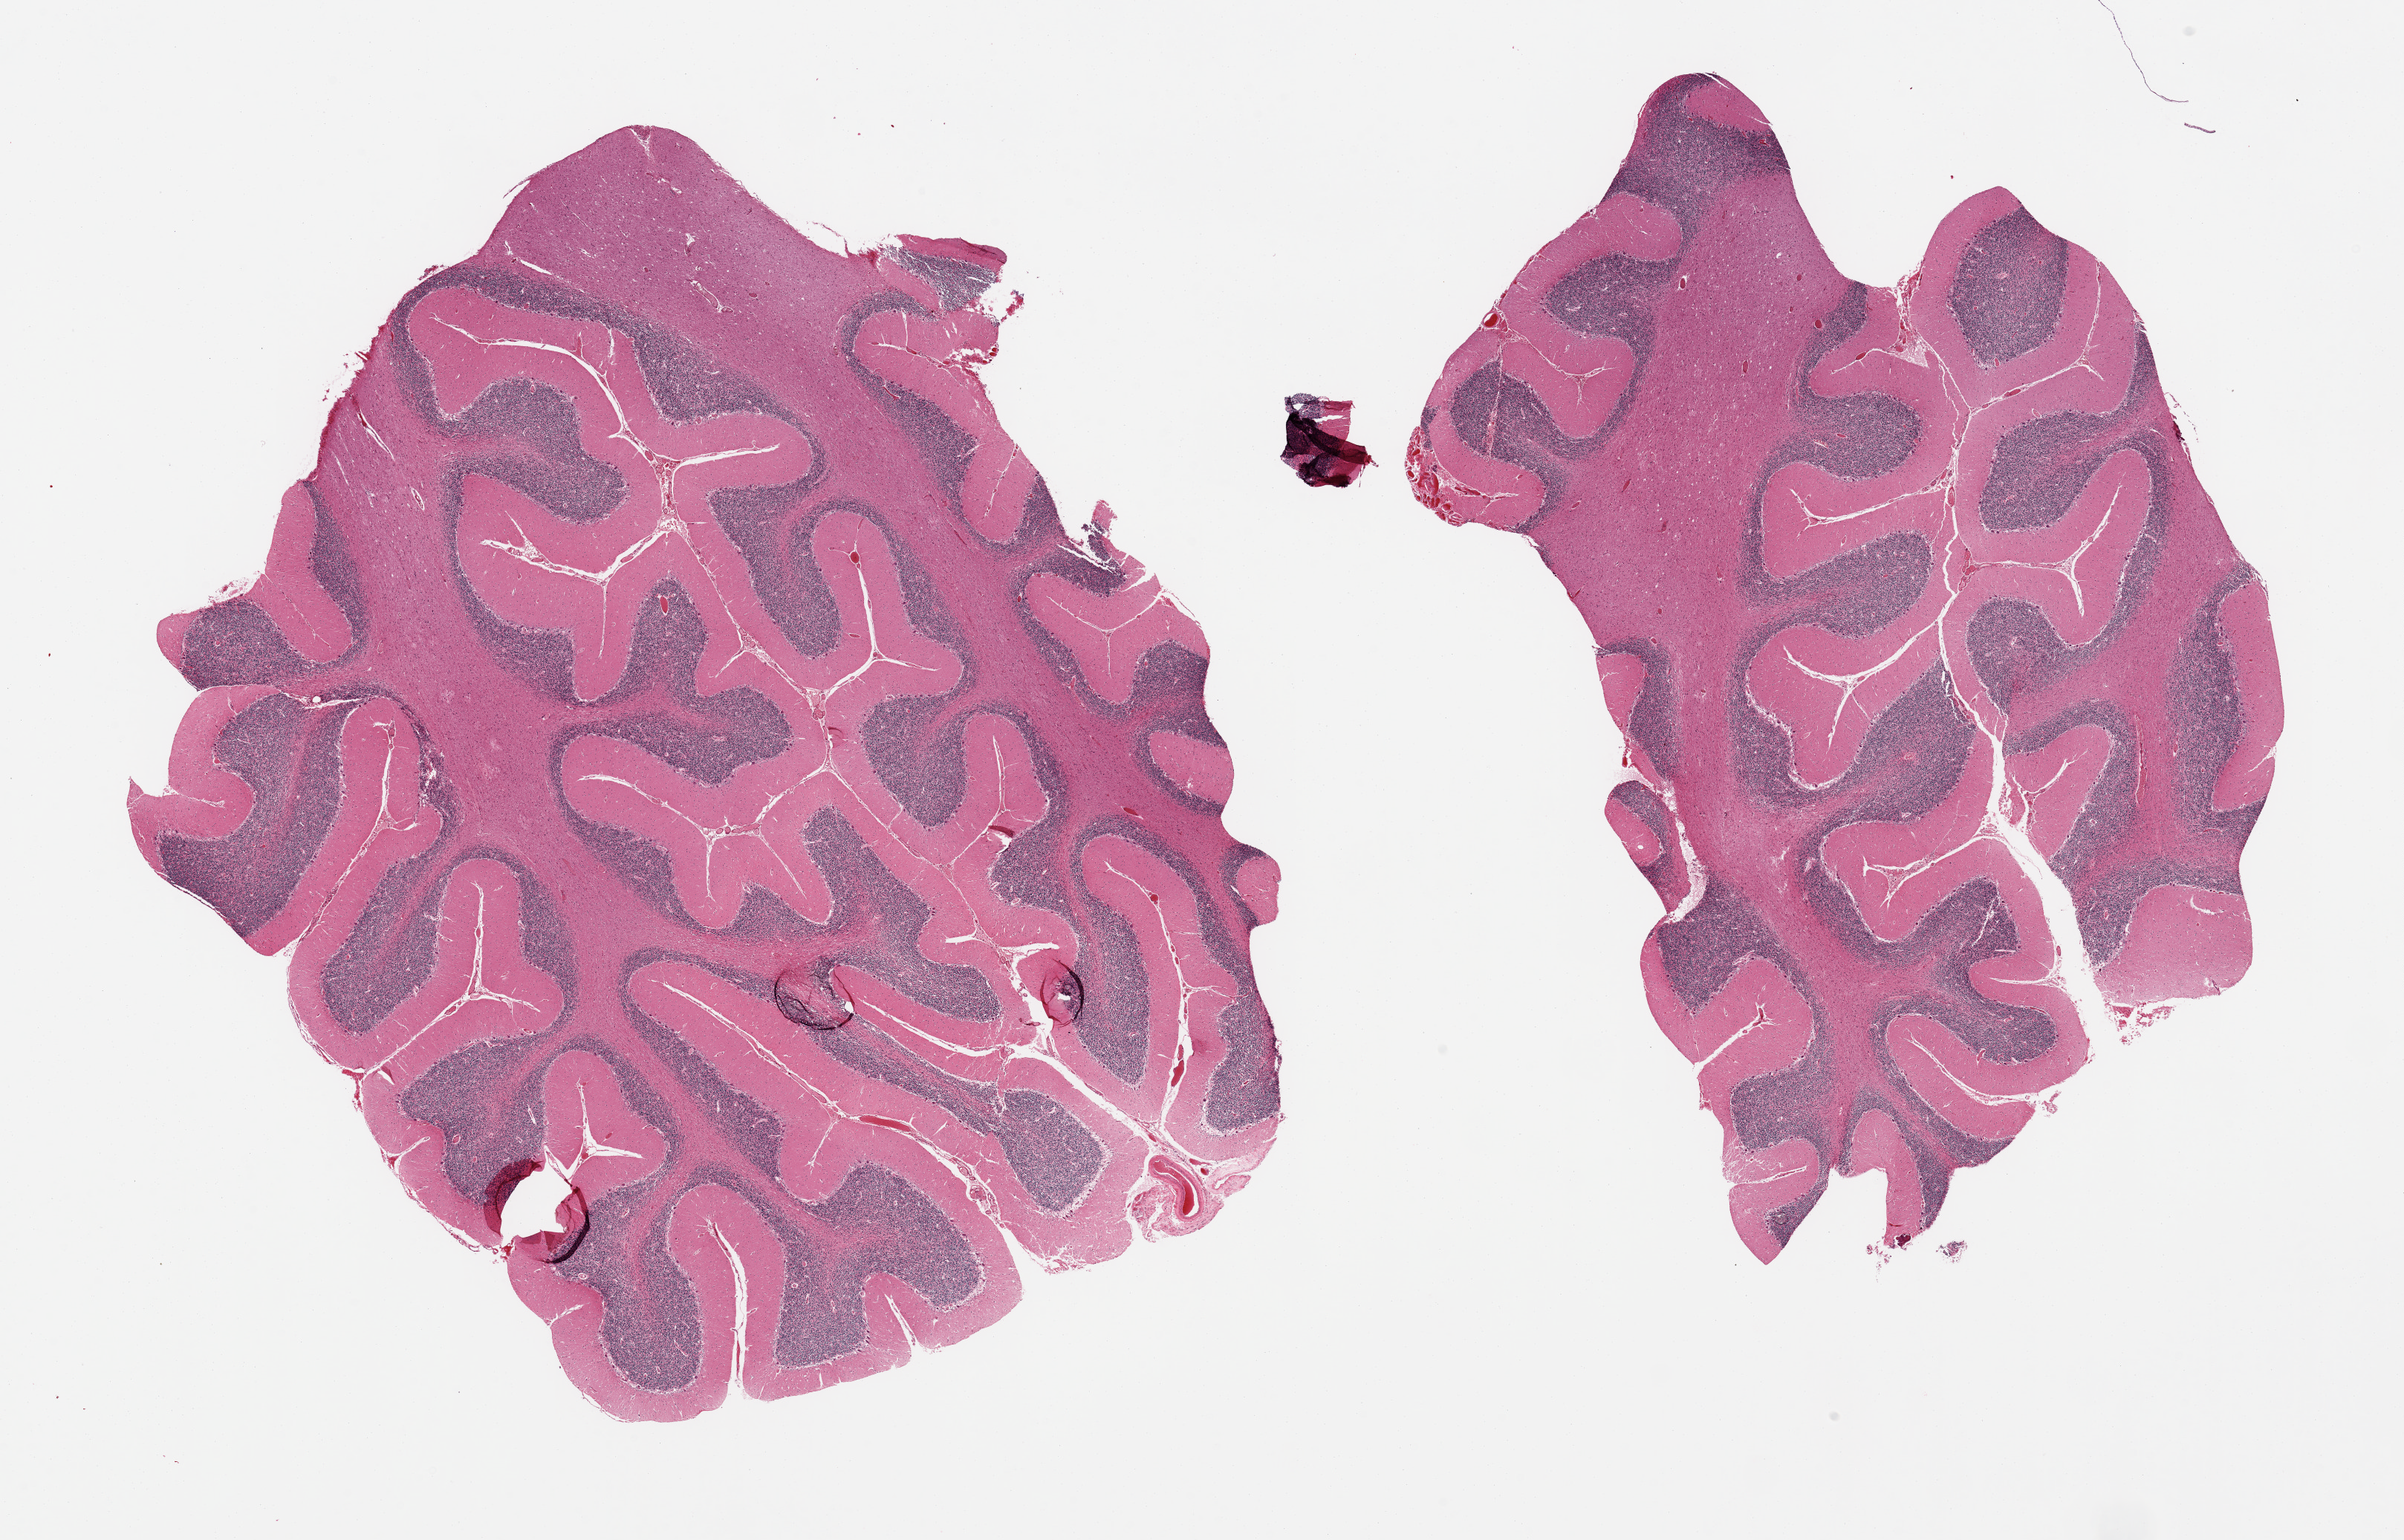
Whole-slide image, hematoxylin and eosin (H&E) stain — whole scanned area (about 25.6 x 16.4 mm) shown as a low-resolution overview, PAXgene-fixed, paraffin-embedded tissue, target tissue: cerebellum, tissue donor sample. Donor sex: male.
Pathologist's review note for this sample: 2 pieces, no abnormalities.